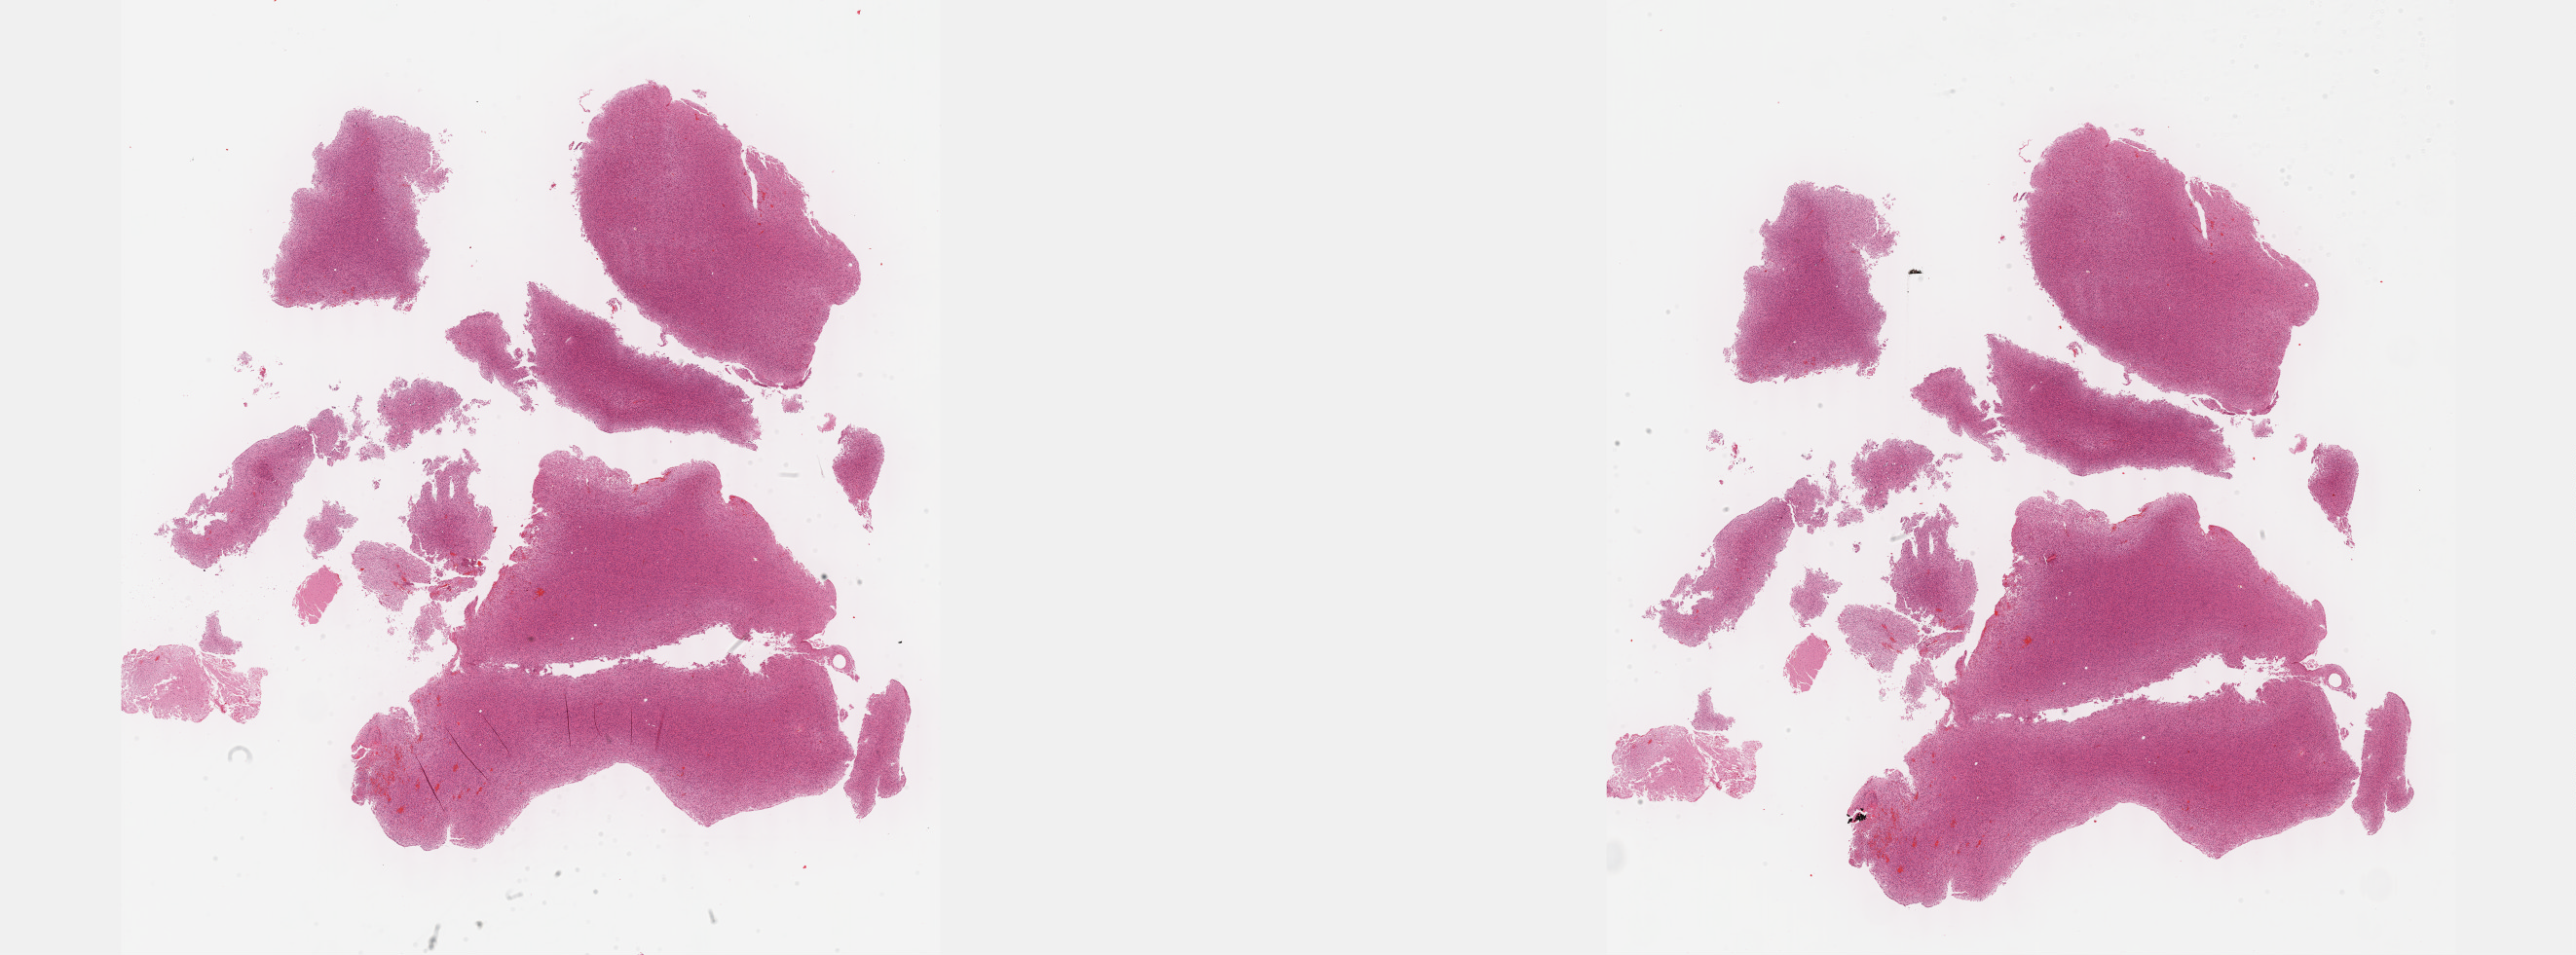
Whole-slide histology image, H&E, whole scanned area (about 42.8 x 15.9 mm) shown as a low-resolution overview. Formalin-fixed paraffin-embedded (FFPE) diagnostic section. Primary tumour sample from the brain. Female, age 43 years at initial diagnosis. Histologic grade: G3 (poorly differentiated).
Diagnosis: Astrocytoma, anaplastic (cerebrum). Laterality: left.